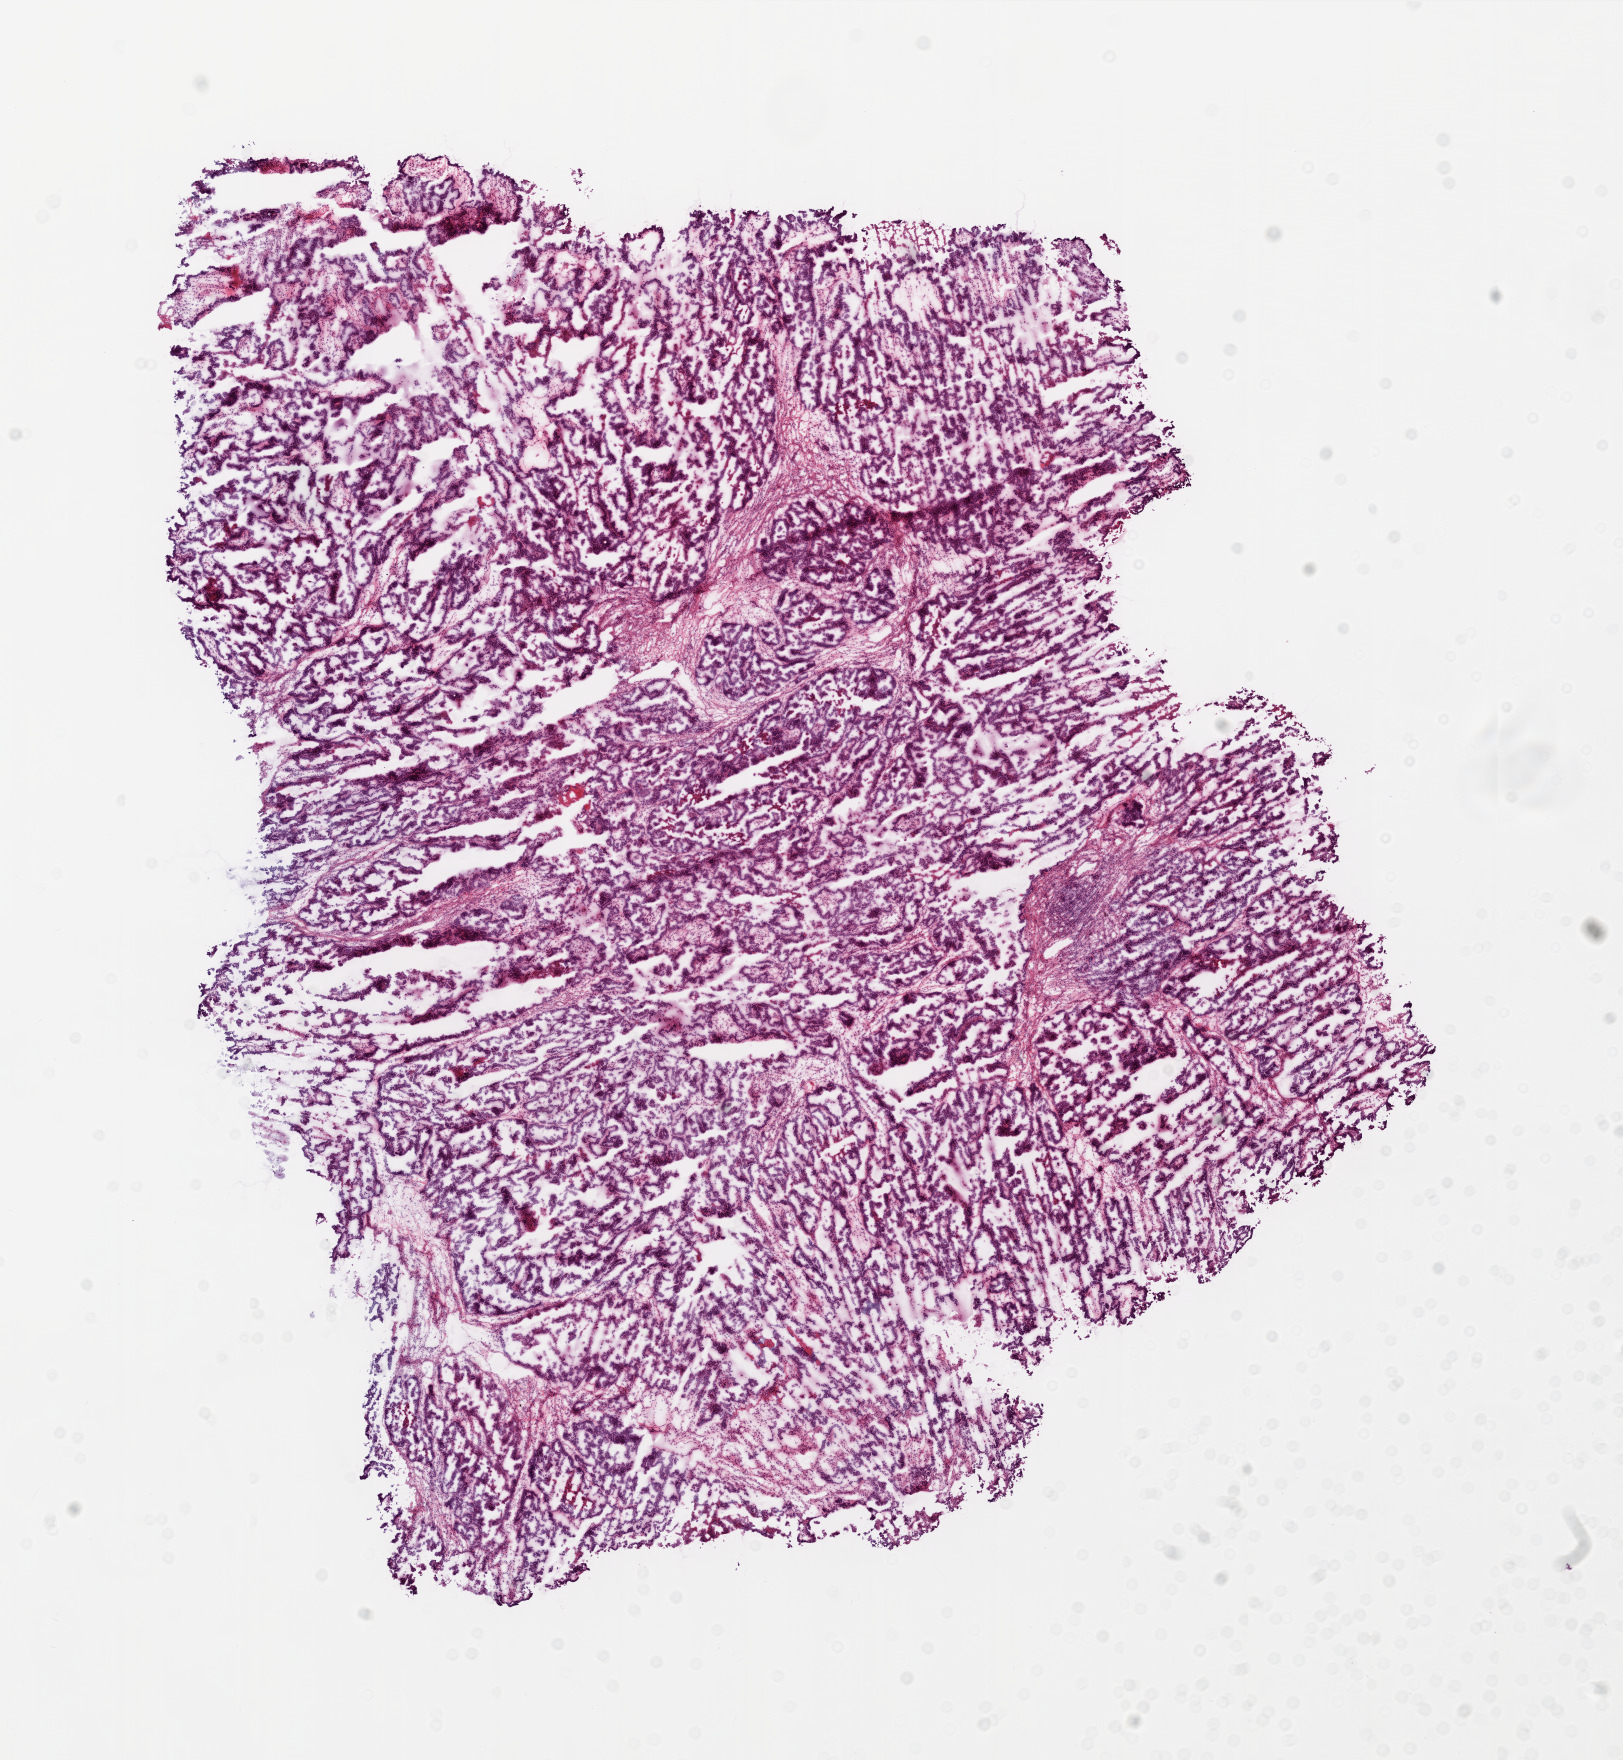
Whole-slide histology image, H&E-stained — whole scanned area (about 13.0 x 14.1 mm) shown as a low-resolution overview, frozen section from the top of the tissue portion, ovary, primary tumour sample. Female patient; age at initial diagnosis 42 years. Histologic grade: G3 (poorly differentiated). Slide review estimates, as recorded: tumour cells 89%, tumour nuclei 90%, normal cells 10%, stromal cells 0%, necrosis 1%.
- laterality: bilateral
- diagnosis: Serous cystadenocarcinoma, NOS
- FIGO stage: IIIC